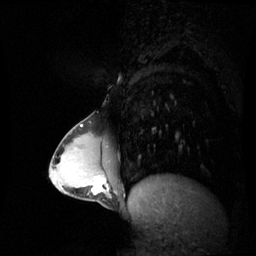
Breast MRI (dynamic contrast-enhanced), one sagittal slice; position 22 of 60 along the scan axis; dynamic contrast-enhanced series, image 2 of 3 at this slice position (ordered by acquisition); 1.5 T; TE 4.2 ms, TR 8.9 ms; 2.4 mm slice thickness; 256 × 256 image matrix, field of view 300 × 300 mm. Patient: female, 34 years. From the clinical record (not read from this slice): setting: breast cancer imaged before/during neoadjuvant chemotherapy; receptor status: triple-negative.
Outlined on this slice (semi-automatic segmentation, software-assisted and operator-edited):
- analysis volume of interest (the breast-tissue region the enhancement analysis was run in; not a lesion): bounding box [x1, y1, x2, y2] px = [65, 168, 107, 201]
- tumour enhancement mask (voxels above the 70 % enhancement threshold inside the analysis volume of interest): [92, 177, 105, 194]